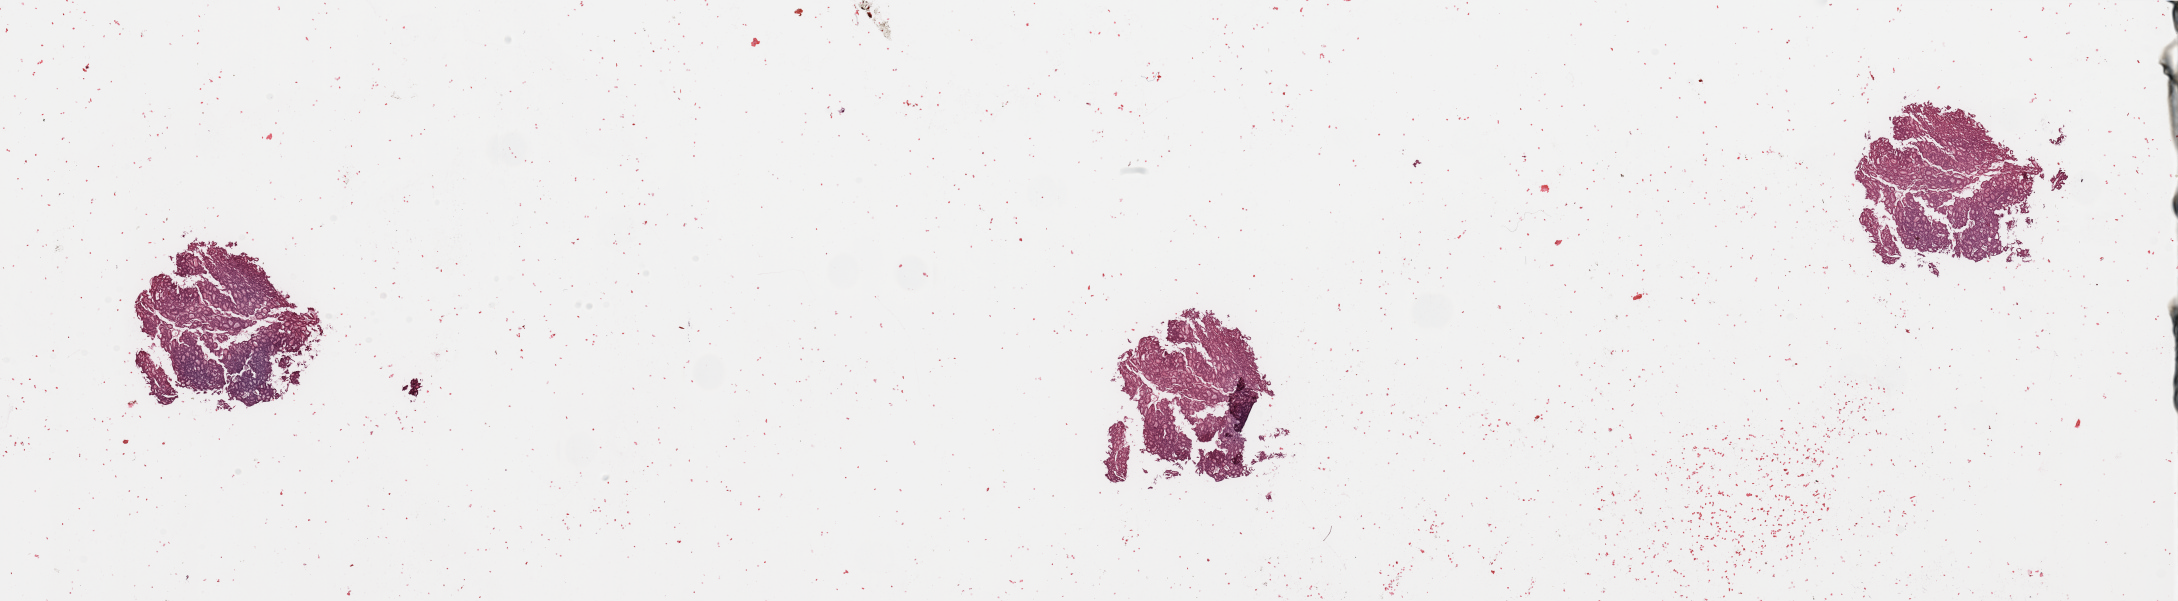
Digitized Hematoxylin and eosin (H&E) stained tissue section (whole slide), whole scanned area (about 34.5 x 9.5 mm, from a 20x scan) shown as a low-resolution overview, tumour tissue sample, uterus. 71-year-old female patient. Histologic grade: G2 (moderately differentiated).
Diagnosis: Endometrioid adenocarcinoma, NOS. Primary tumour site (as recorded): anterior endometrium. AJCC pathologic stage: I.